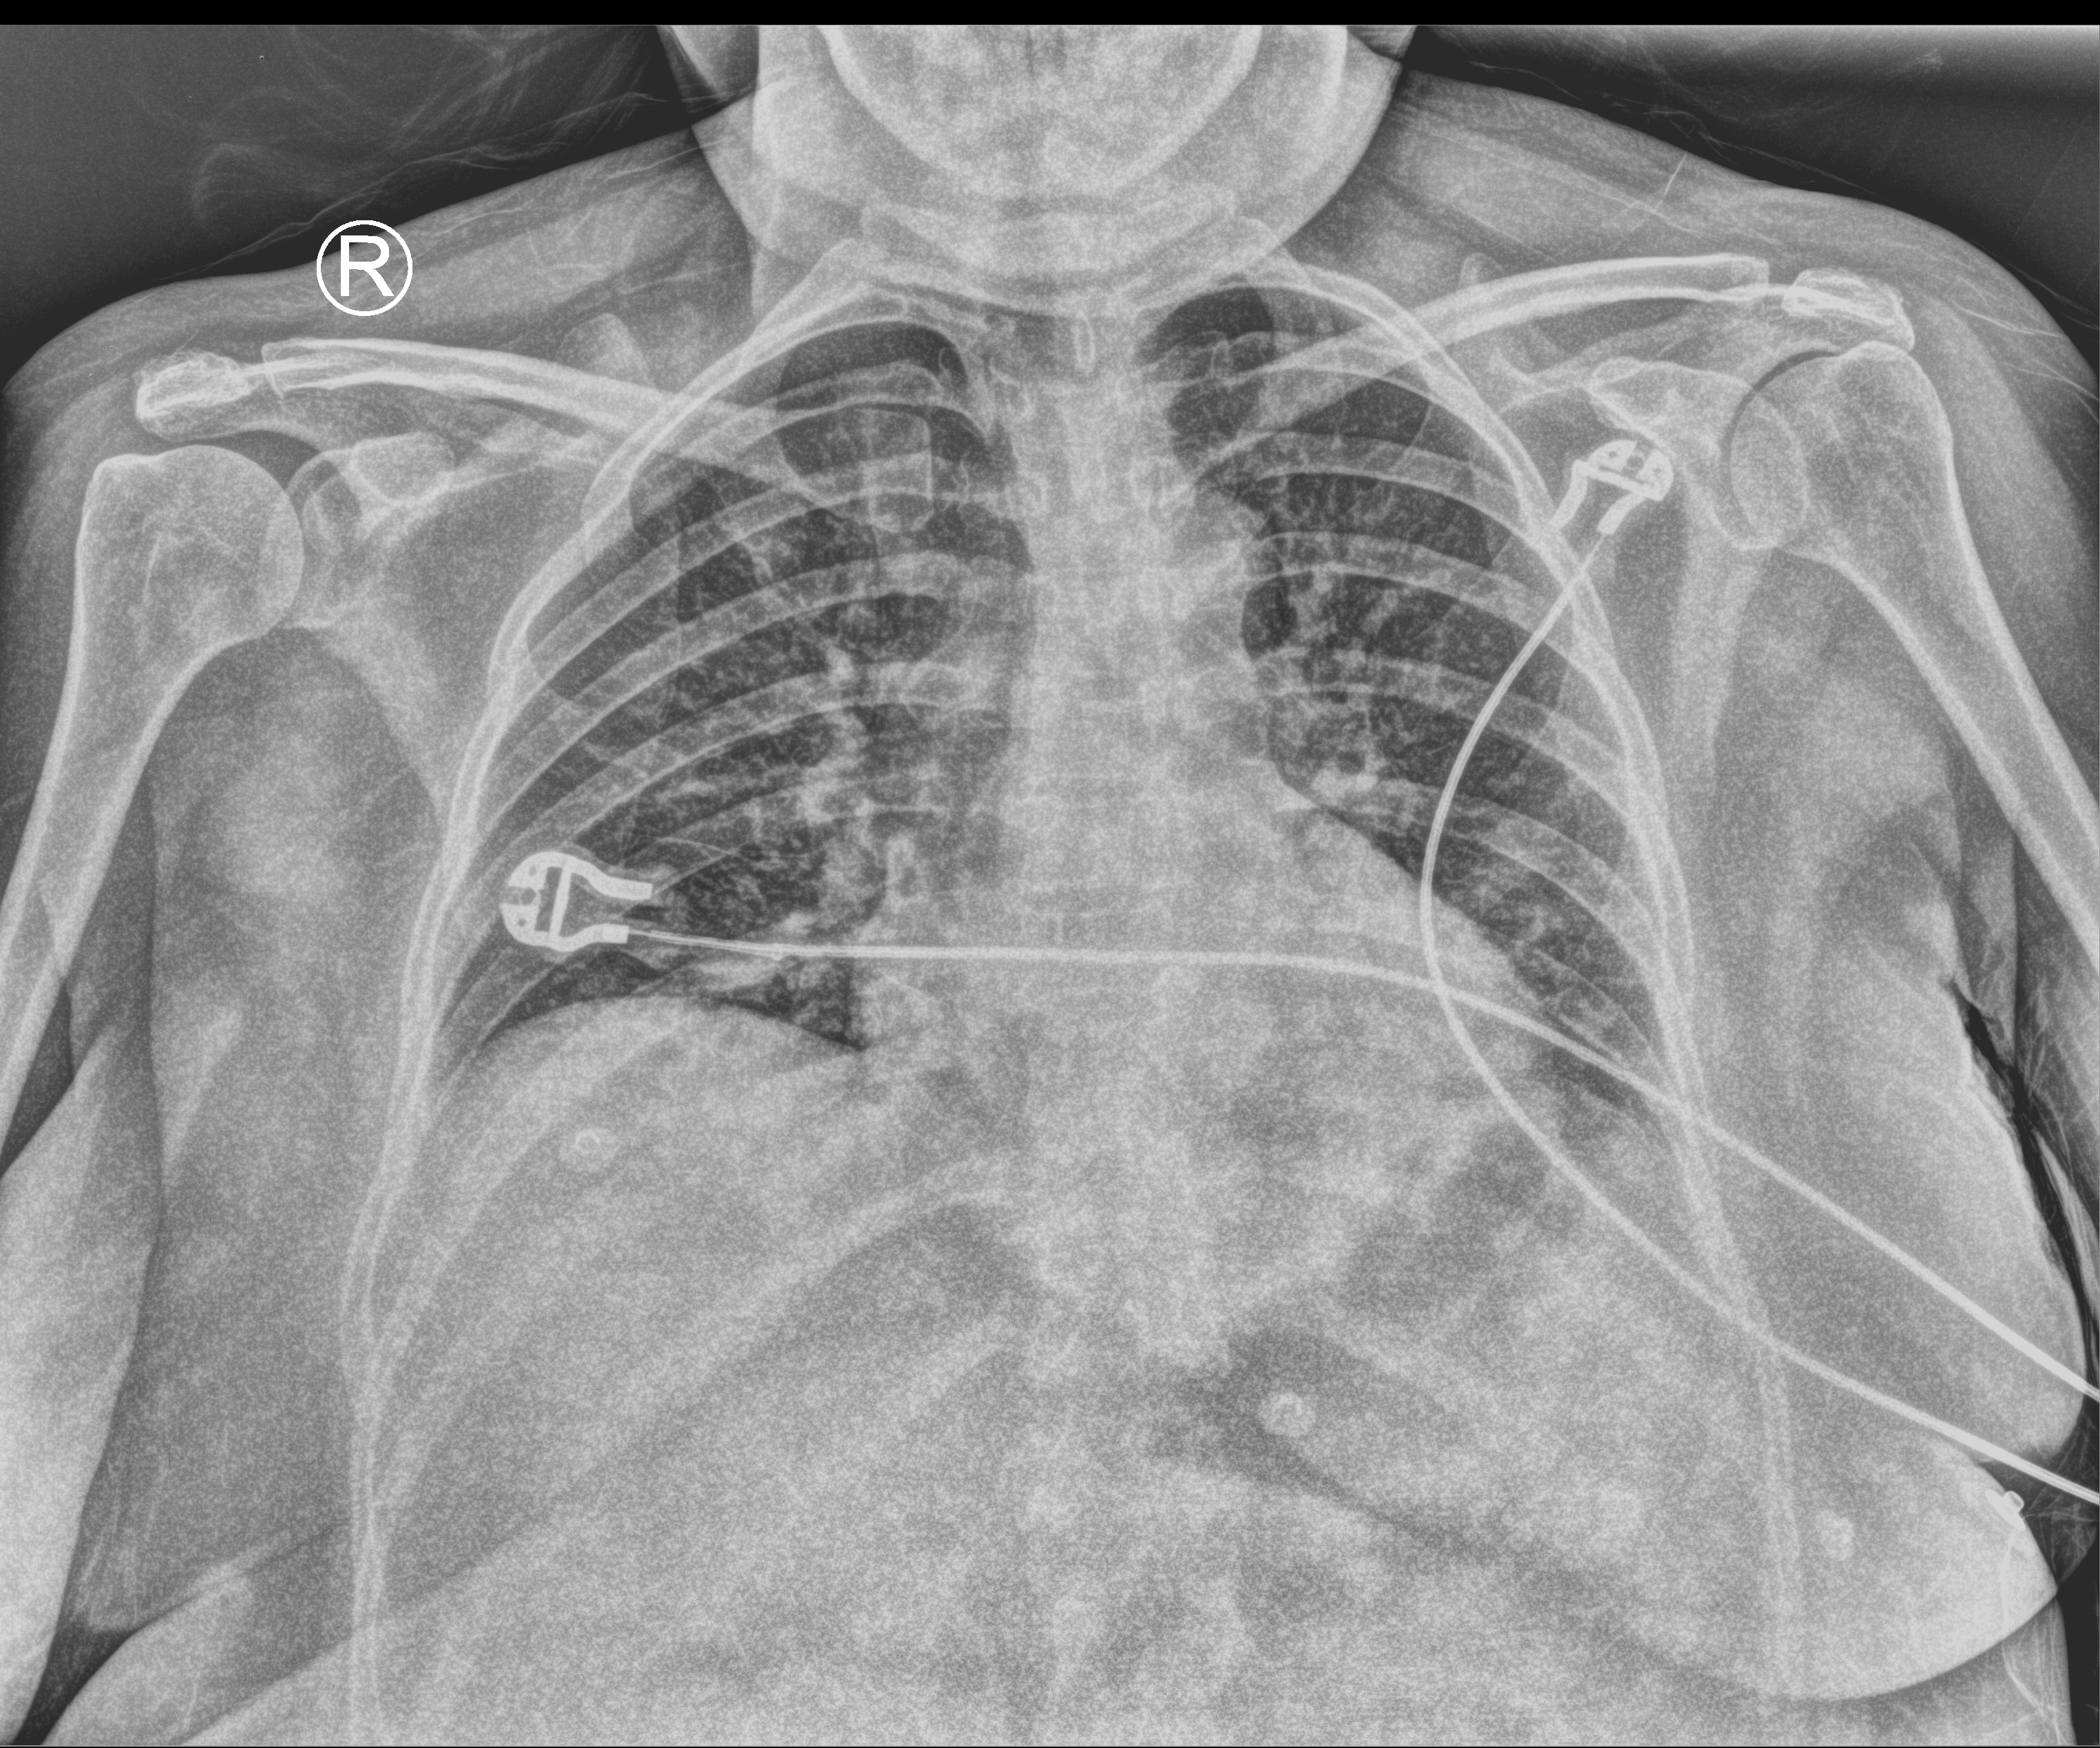
Chest X-ray (portable); anteroposterior (AP) projection. Patient hospitalised with COVID-19; female, aged 18–59 years.
From the hospital-stay record, not from the radiograph (when in the stay this image was taken is not recorded): mechanically ventilated during this hospital stay: no.